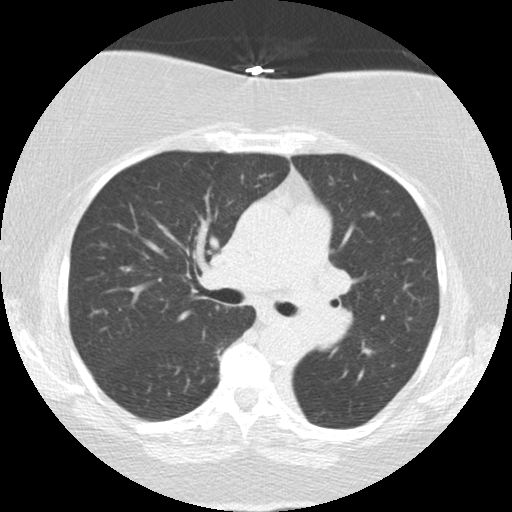
Low-dose screening chest CT, one axial slice. Slice 82 of 136 in the series (ordered by position). Reconstruction kernel STANDARD. Lung window (W 1500 / L -600 HU). 2.5 mm slice thickness. 512 × 512 image matrix, field of view 309 × 309 mm.
Annotated regions visible in this slice (manually delineated by an expert):
- lesion 2 (tumor, mediastinum): box from (x=290, y=265) to (x=355, y=346) px